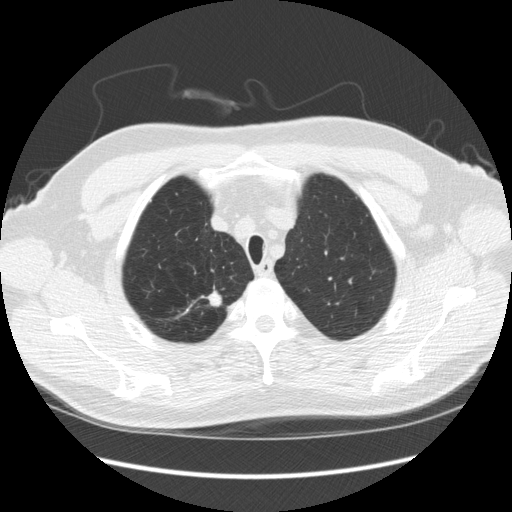
Axial slice from a low-dose chest CT screening exam. Third screening round (two years after baseline). Lung window (W 1500 / L -600 HU). Slice 32 of 248 in the series. Male, age 64 years at enrolment. Former smoker at enrolment.
- Expert-annotated lung lesion, bounding box (x1, y1, x2, y2) in pixels: (192, 283, 230, 317).
- The screening reader recorded 4 non-calcified nodules or masses ≥4 mm on this exam (right upper lobe, right upper lobe, right upper lobe, right upper lobe); which of them this box marks is not recorded.
- Official screen result: positive, other.
- Lung cancer was diagnosed 15 days after this screen: adenocarcinoma, NOS, right upper lobe, moderately differentiated (G2), stage IA (AJCC 6th edition), 14 mm at pathology.